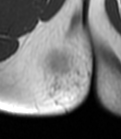
MRI of an extremity soft-tissue mass, one axial slice. Position 13 of 47 along the scan axis. MR volume resampled by the dataset authors to the PET/CT grid (not the native acquisition matrix). 121 × 139 image matrix, field of view 118 × 136 mm. Female patient. From the clinical record (not read from this slice): histological type: epithelioid sarcoma; grade: intermediate; site of the primary tumour: right buttock.
Annotated regions visible in this slice (expert contour drawn on MRI and transferred to this co-registered scan by the dataset authors):
- gross tumour volume including surrounding oedema: bounding box (x1, y1, x2, y2) in pixels: (43, 48, 90, 110)
- gross tumour volume (mass): (59, 59, 67, 71)